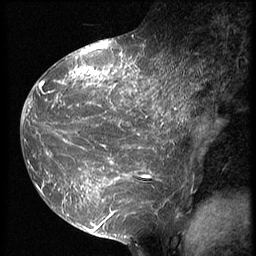
Breast MRI (dynamic contrast-enhanced), one sagittal slice; position 28 of 64 along the scan axis; 3 images stored at this slice position (order not interpretable as contrast timing); 1.5 T; TE 4.2 ms, TR 9 ms; 2.5 mm slice thickness; 256 × 256 image matrix. Female patient, age 39 years. Case-level facts recorded for this patient, not image findings: setting: breast cancer imaged before/during neoadjuvant chemotherapy; receptor status: HER2-positive.
Structures marked on this image (semi-automatically segmented with operator editing):
- analysis volume of interest (the breast-tissue region the enhancement analysis was run in; not a lesion): bounding box [x1, y1, x2, y2] px = [23, 47, 188, 239]
- tumour enhancement mask (voxels above the 140 % enhancement threshold inside the analysis volume of interest): [23, 47, 188, 230]